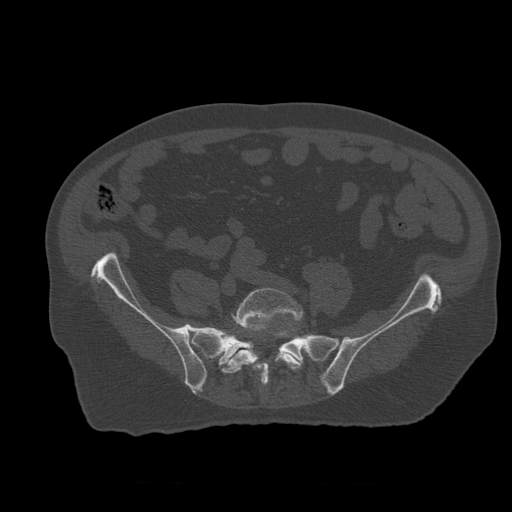
CT including the spine, one axial slice; position 132 of 399 along the scan axis; reconstruction kernel STANDARD; bone window (W 1800 / L 400 HU); 1.25 mm slice thickness; 512 × 512 image matrix. Patient age 73 years. Case-level facts recorded for this patient, not image findings: primary cancer: prostate; vertebrae with lytic lesions (as recorded): L2.
Annotated regions visible in this slice (semi-automatically segmented with operator editing):
- L5 vertebra: bounding box (x1, y1, x2, y2) in pixels: (222, 288, 303, 387)